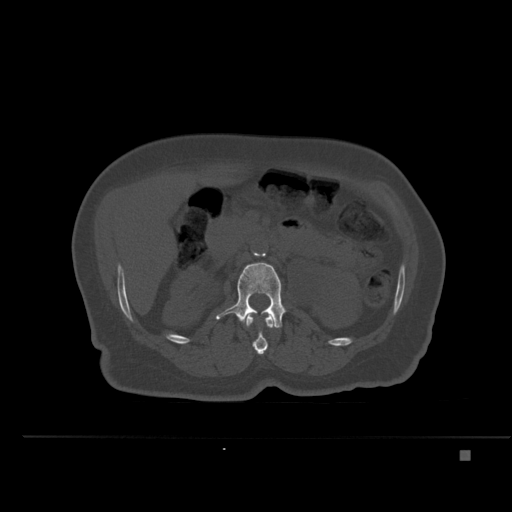
CT including the spine, one axial slice; slice 221 of 477 in the series (ordered by position); bone window (W 1800 / L 400 HU); 1.5 mm slice thickness; 512 × 512 image matrix, field of view 422 × 422 mm. Female patient, age 74 years. Case-level facts recorded for this patient, not image findings: primary cancer: colon.
Outlined on this slice (semi-automatically segmented with operator editing):
- L1 vertebra: bounding box [x1, y1, x2, y2] px = [245, 313, 275, 355]
- L2 vertebra: [216, 262, 286, 328]